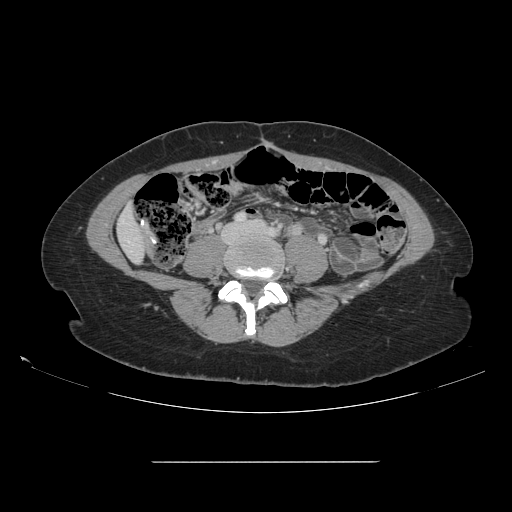
Contrast-enhanced abdominal CT, one axial slice; position 13 of 151 along the scan axis; intravenous contrast given; soft-tissue window (W 400 / L 40 HU); 2.5 mm slice thickness; 512 × 512 image matrix. Female patient, age 46 years. Case-level facts recorded for this patient, not image findings: diagnosis: colorectal cancer liver metastases, imaged before liver resection.
Structures marked on this image (expert manual segmentation):
- liver: box from (x=118, y=208) to (x=146, y=261) px
- planned liver remnant (the part of the liver to remain after resection): (x=119, y=209)–(x=146, y=261)